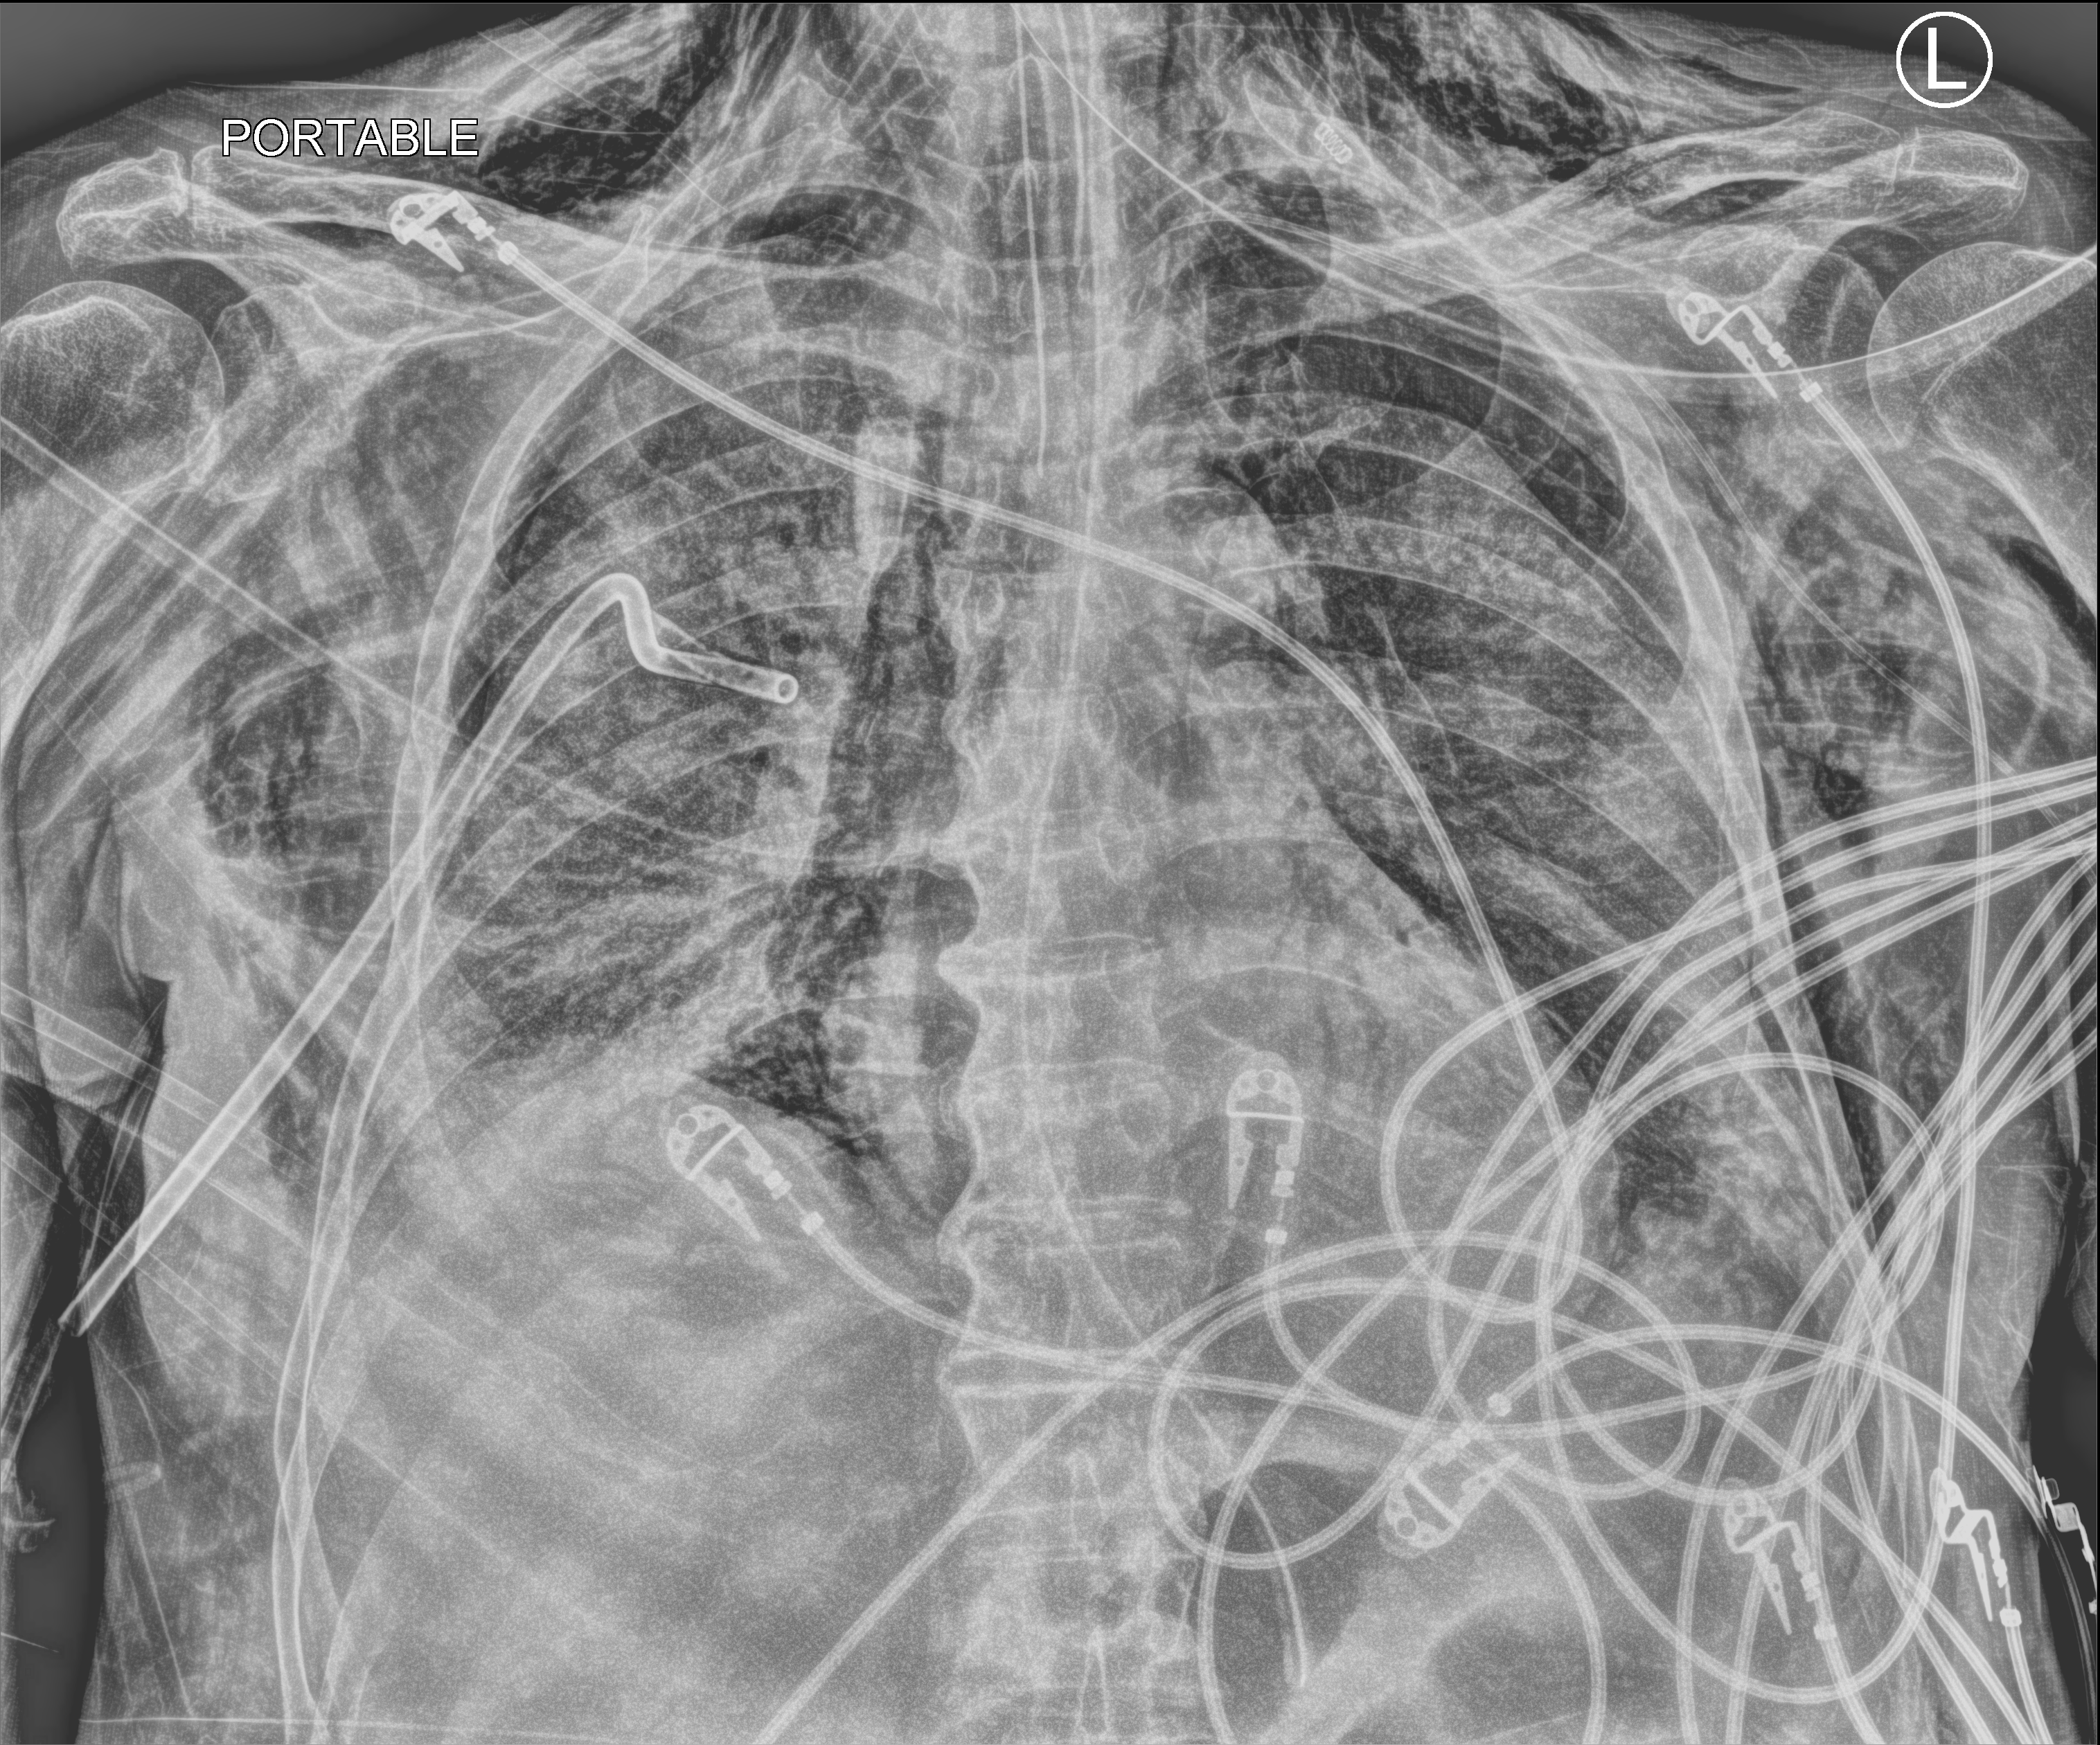
Chest X-ray (portable). Male patient hospitalised with COVID-19, age 75–90 years.
From the hospital-stay record, not from the radiograph (when in the stay this image was taken is not recorded): admitted to intensive care during this hospital stay: yes.